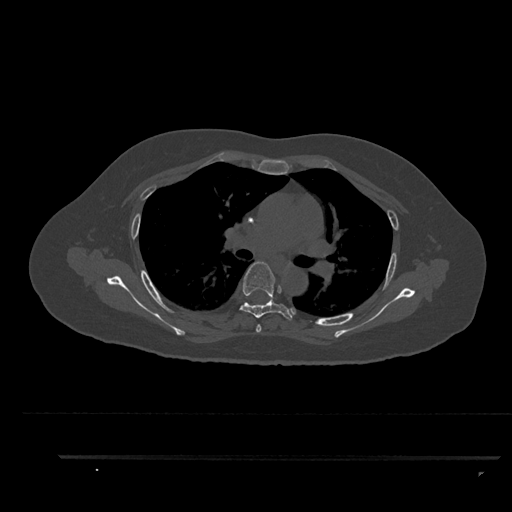
CT including the spine, one axial slice. Position 604 of 797 along the scan axis. Reconstruction kernel Br40s/3. Bone window (W 1800 / L 400 HU). 0.5 mm slice thickness. 512 × 512 image matrix. Patient: female, 44 years. Case-level facts recorded for this patient, not image findings: primary cancer: renal.
Outlined on this slice (semi-automatic segmentation, software-assisted and operator-edited):
- T4 vertebra: bounding box (x1, y1, x2, y2) in pixels: (256, 324, 262, 333)
- T5 vertebra: (228, 261, 293, 320)